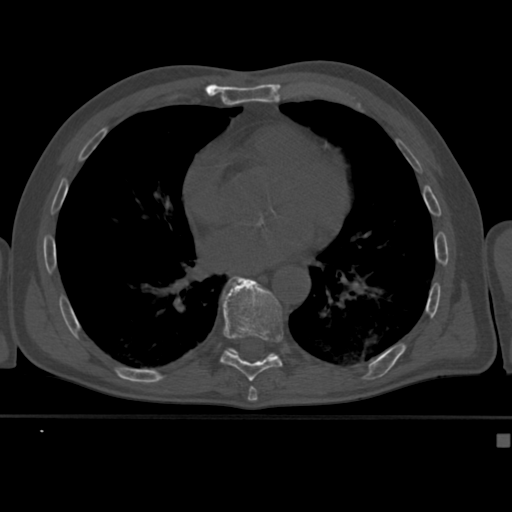
CT including the spine, one axial slice. Slice 244 of 430 in the series (ordered by position). Reconstruction kernel Br40s. Bone window (W 1800 / L 400 HU). 1.5 mm slice thickness. 512 × 512 image matrix. Male patient, age 64 years. From the clinical record (not read from this slice): primary cancer: uterus.
Structures marked on this image (semi-automatic segmentation, software-assisted and operator-edited):
- T10 vertebra: bounding box [x1, y1, x2, y2] px = [228, 348, 238, 354]
- T9 vertebra: [220, 276, 283, 382]